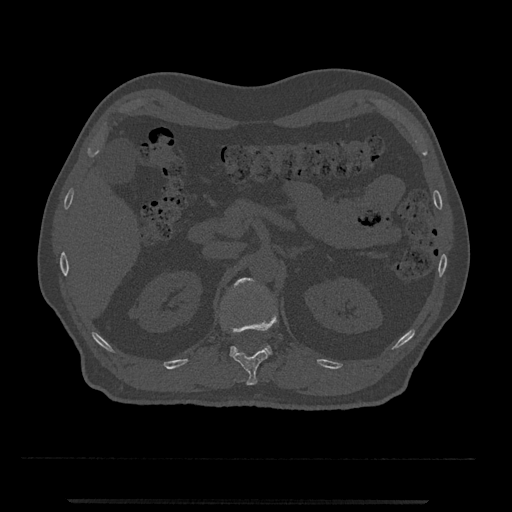
CT including the spine, one axial slice. Position 375 of 797 along the scan axis. Reconstruction kernel Br40s/3. Bone window (W 1800 / L 400 HU). 0.5 mm slice thickness. 512 × 512 image matrix, field of view 419 × 419 mm. Patient: male, 63 years. From the clinical record (not read from this slice): primary cancer: prostate.
Structures marked on this image (semi-automatically segmented with operator editing):
- L1 vertebra: box from (x=230, y=278) to (x=272, y=356) px
- T12 vertebra: (x=230, y=314)–(x=279, y=385)